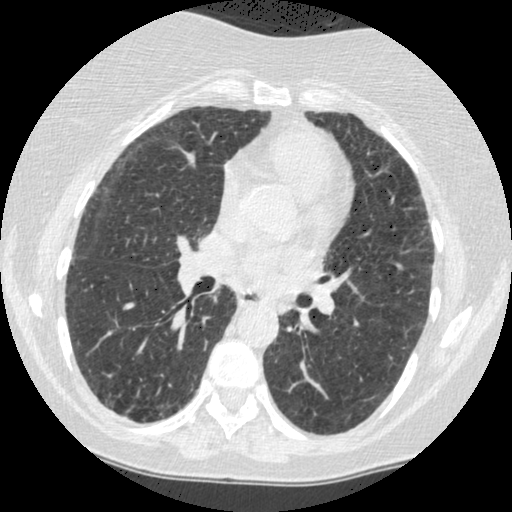
Axial slice from a low-dose chest CT screening exam. First (baseline) screen. Lung window (W 1500 / L -600 HU). 1.25 mm slice thickness. Slice 214 of 442 in the series. 512 × 512 image matrix. Female, age 60 years at enrolment. Former smoker at enrolment.
Lesion marked by an expert reader, bounding box [x1, y1, x2, y2] px = [261, 287, 305, 328]. The screening reader recorded 2 non-calcified nodules or masses ≥4 mm on this exam; which of them this box marks is not recorded. Official screen result: positive, change unspecified: nodule(s) >= 4 mm or enlarging nodule(s), mass(es), or other non-specific abnormalities suspicious for lung cancer. Later outcome: lung cancer diagnosed 794 days after this screen — small cell carcinoma, NOS, left lower lobe, undifferentiated (G4), stage IV (AJCC 6th edition), 69 mm at pathology.